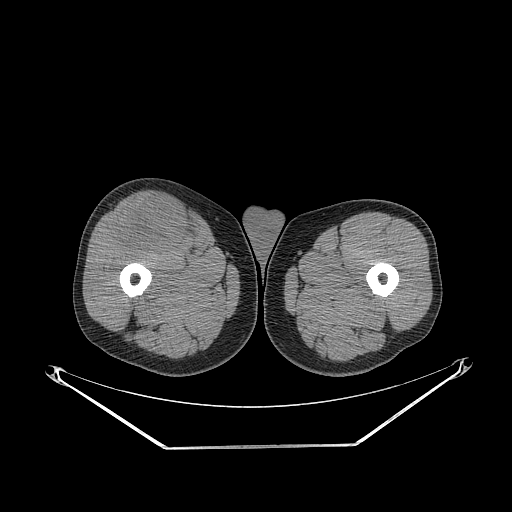
CT of an extremity soft-tissue mass (from a PET/CT study), one axial slice. Position 274 of 311 along the scan axis. Reconstruction kernel STANDARD. Soft-tissue window (W 400 / L 40 HU). 512 × 512 image matrix, field of view 500 × 500 mm. Male patient. Case-level facts recorded for this patient, not image findings: histological type: pleiomorphic leiomyosarcoma; grade: intermediate; site of the primary tumour: right thigh.
Structures marked on this image (expert contour drawn on MRI and transferred to this co-registered scan by the dataset authors):
- gross tumour volume including surrounding oedema: bounding box (x1, y1, x2, y2) in pixels: (116, 199, 191, 255)
- gross tumour volume (mass): (116, 199, 191, 255)